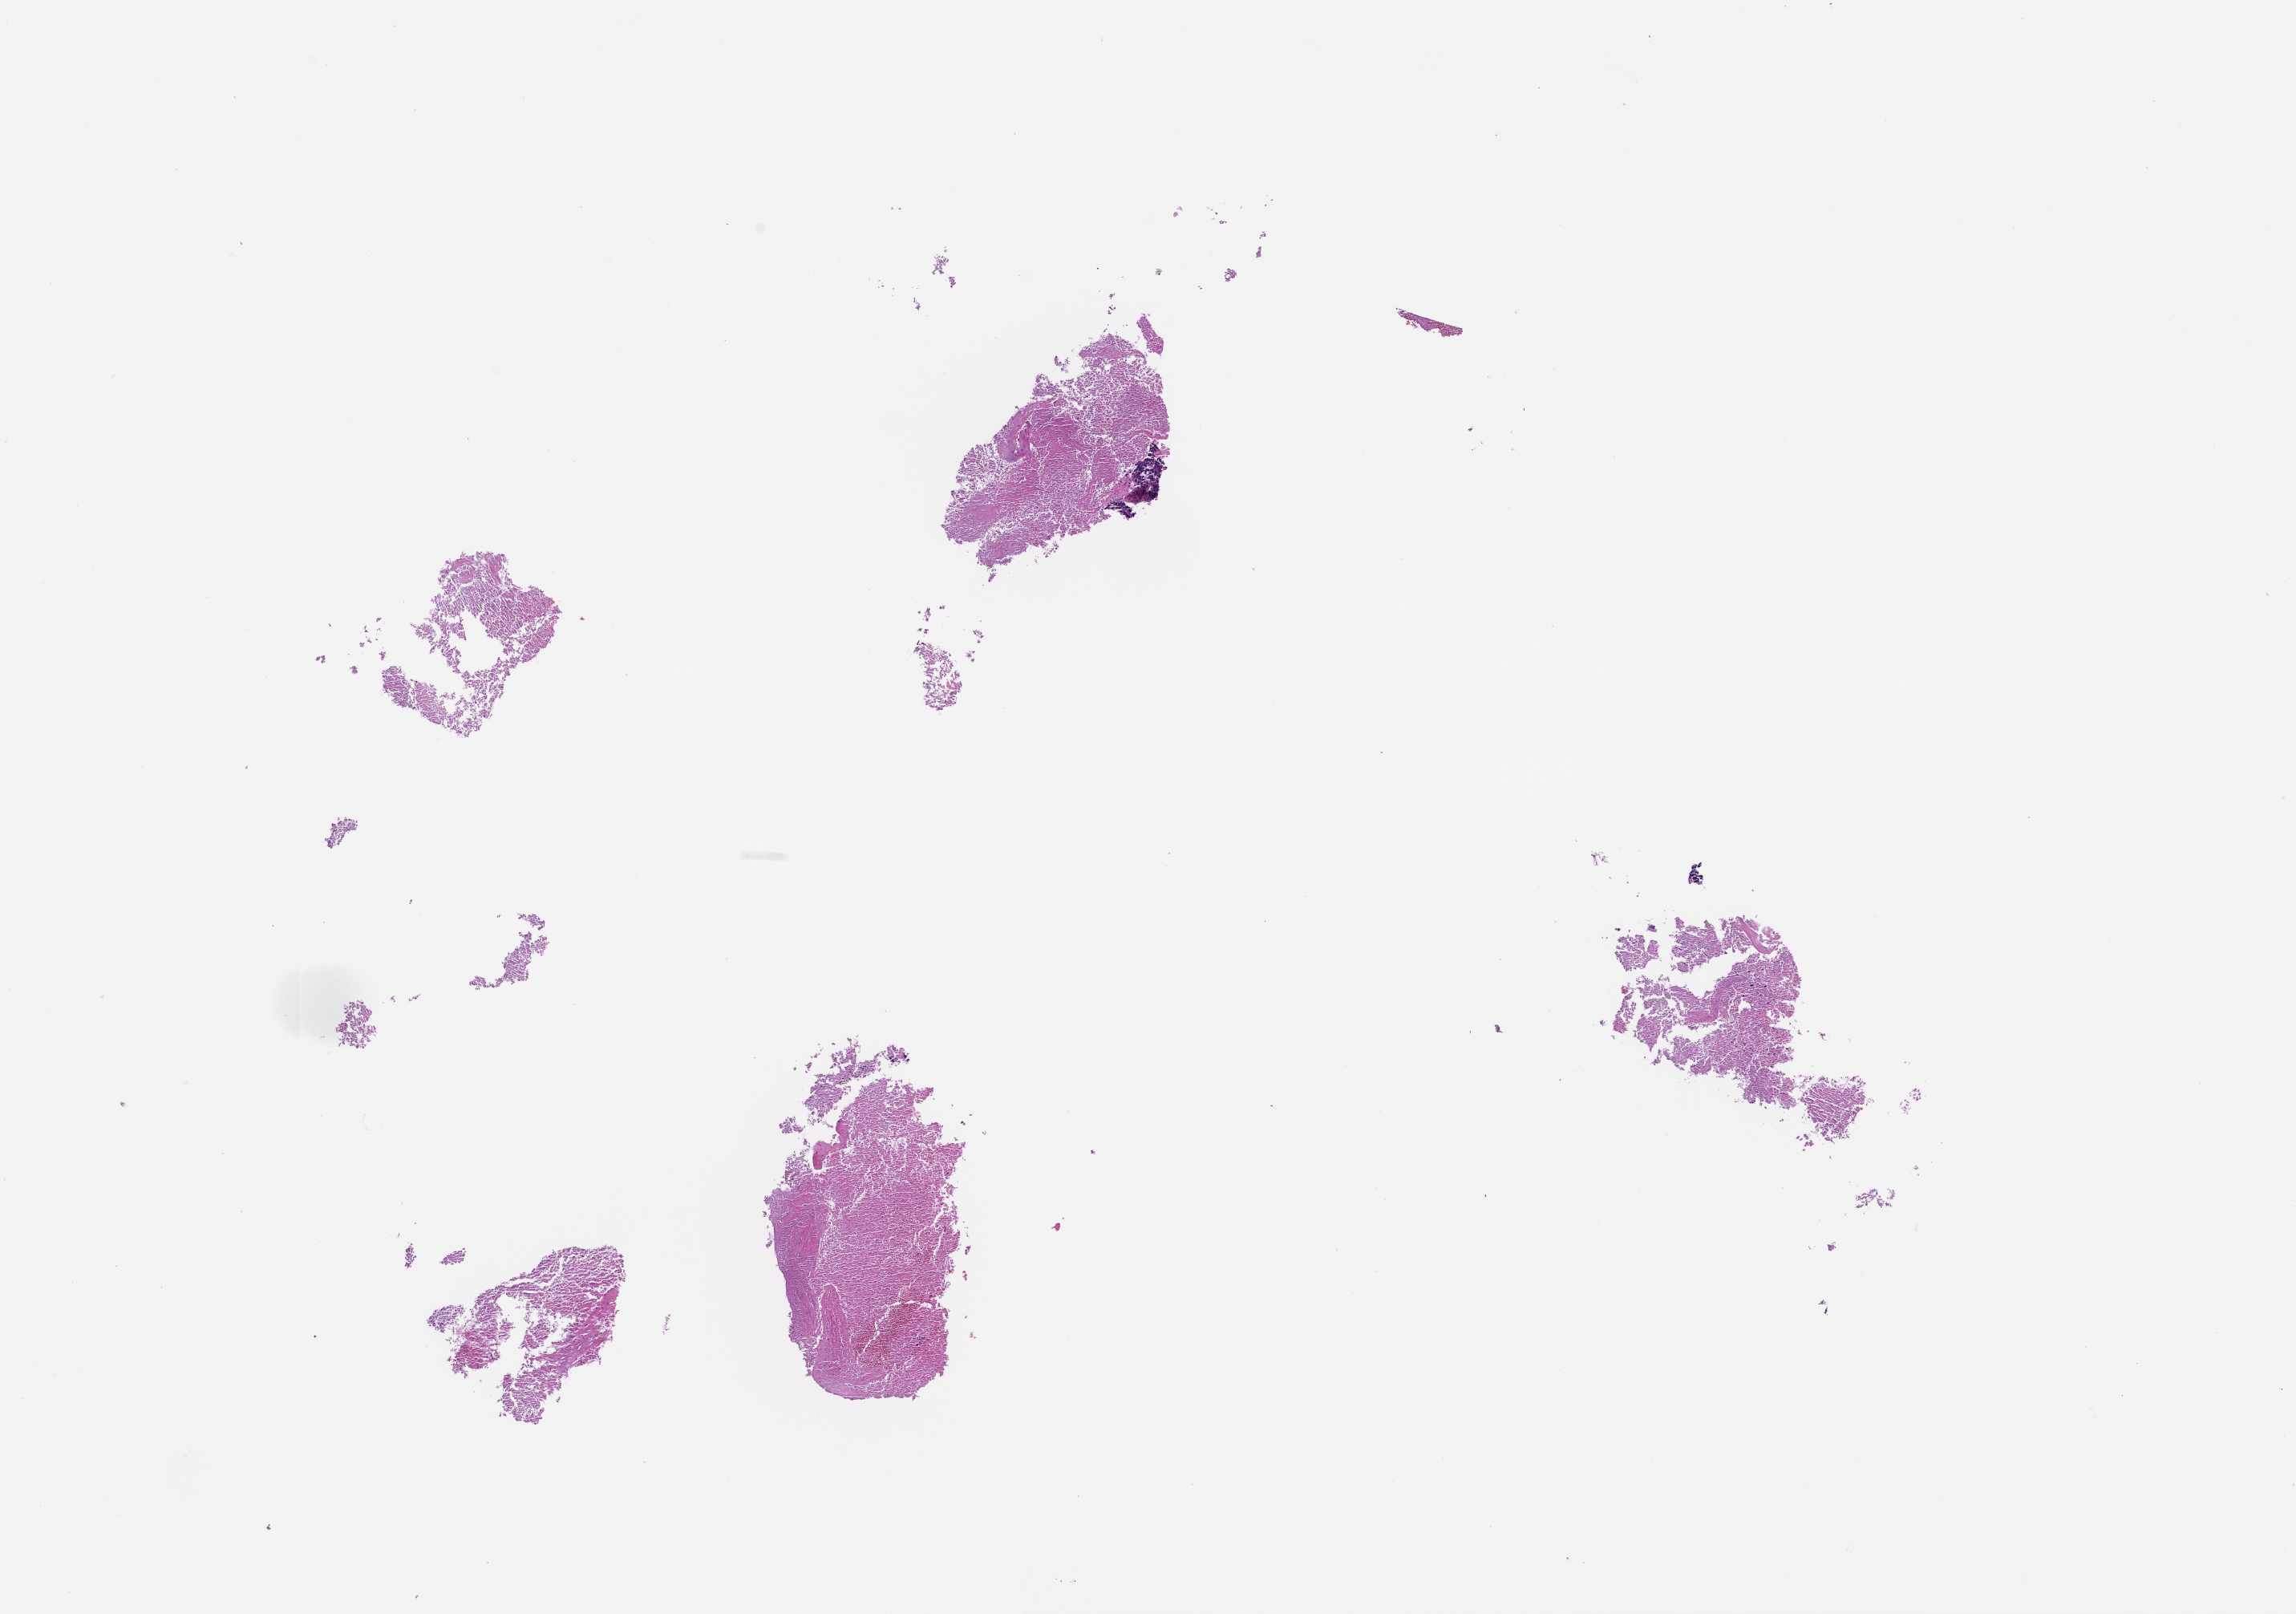
Whole-slide image, haematoxylin and eosin stain — shown as a low-resolution overview of the whole scanned area (about 11.6 x 8.1 mm); formalin-fixed paraffin-embedded section; tissue site: lung. Patient sex: female.
• this section: primary tumor
• diagnosis: Non-Small Cell Lung Carcinoma